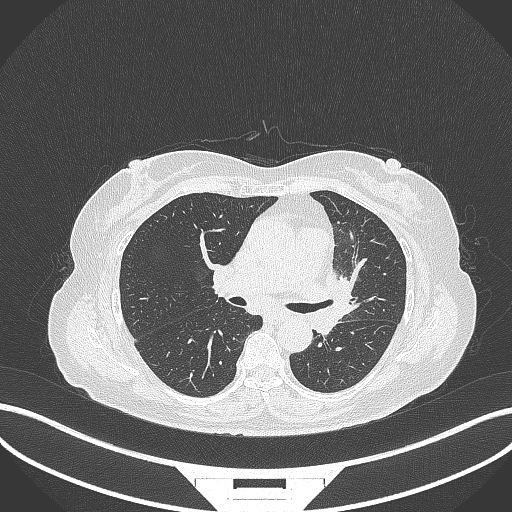
Chest CT, one axial slice; slice 192 of 382 in the series (ordered by position); reconstruction kernel B70f; lung window (W 1500 / L -600 HU); 1 mm slice thickness; 512 × 512 image matrix, field of view 400 × 400 mm. Female patient, age 64 years. Case-level facts recorded for this patient, not image findings: clinical TNM (as recorded): T2a N2 M0.
Structures marked on this image (rectangle marked by the reading radiologist):
- lung tumour (recorded histology: adenocarcinoma): bounding box <320,269,358,336> (left, top, right, bottom; pixels)